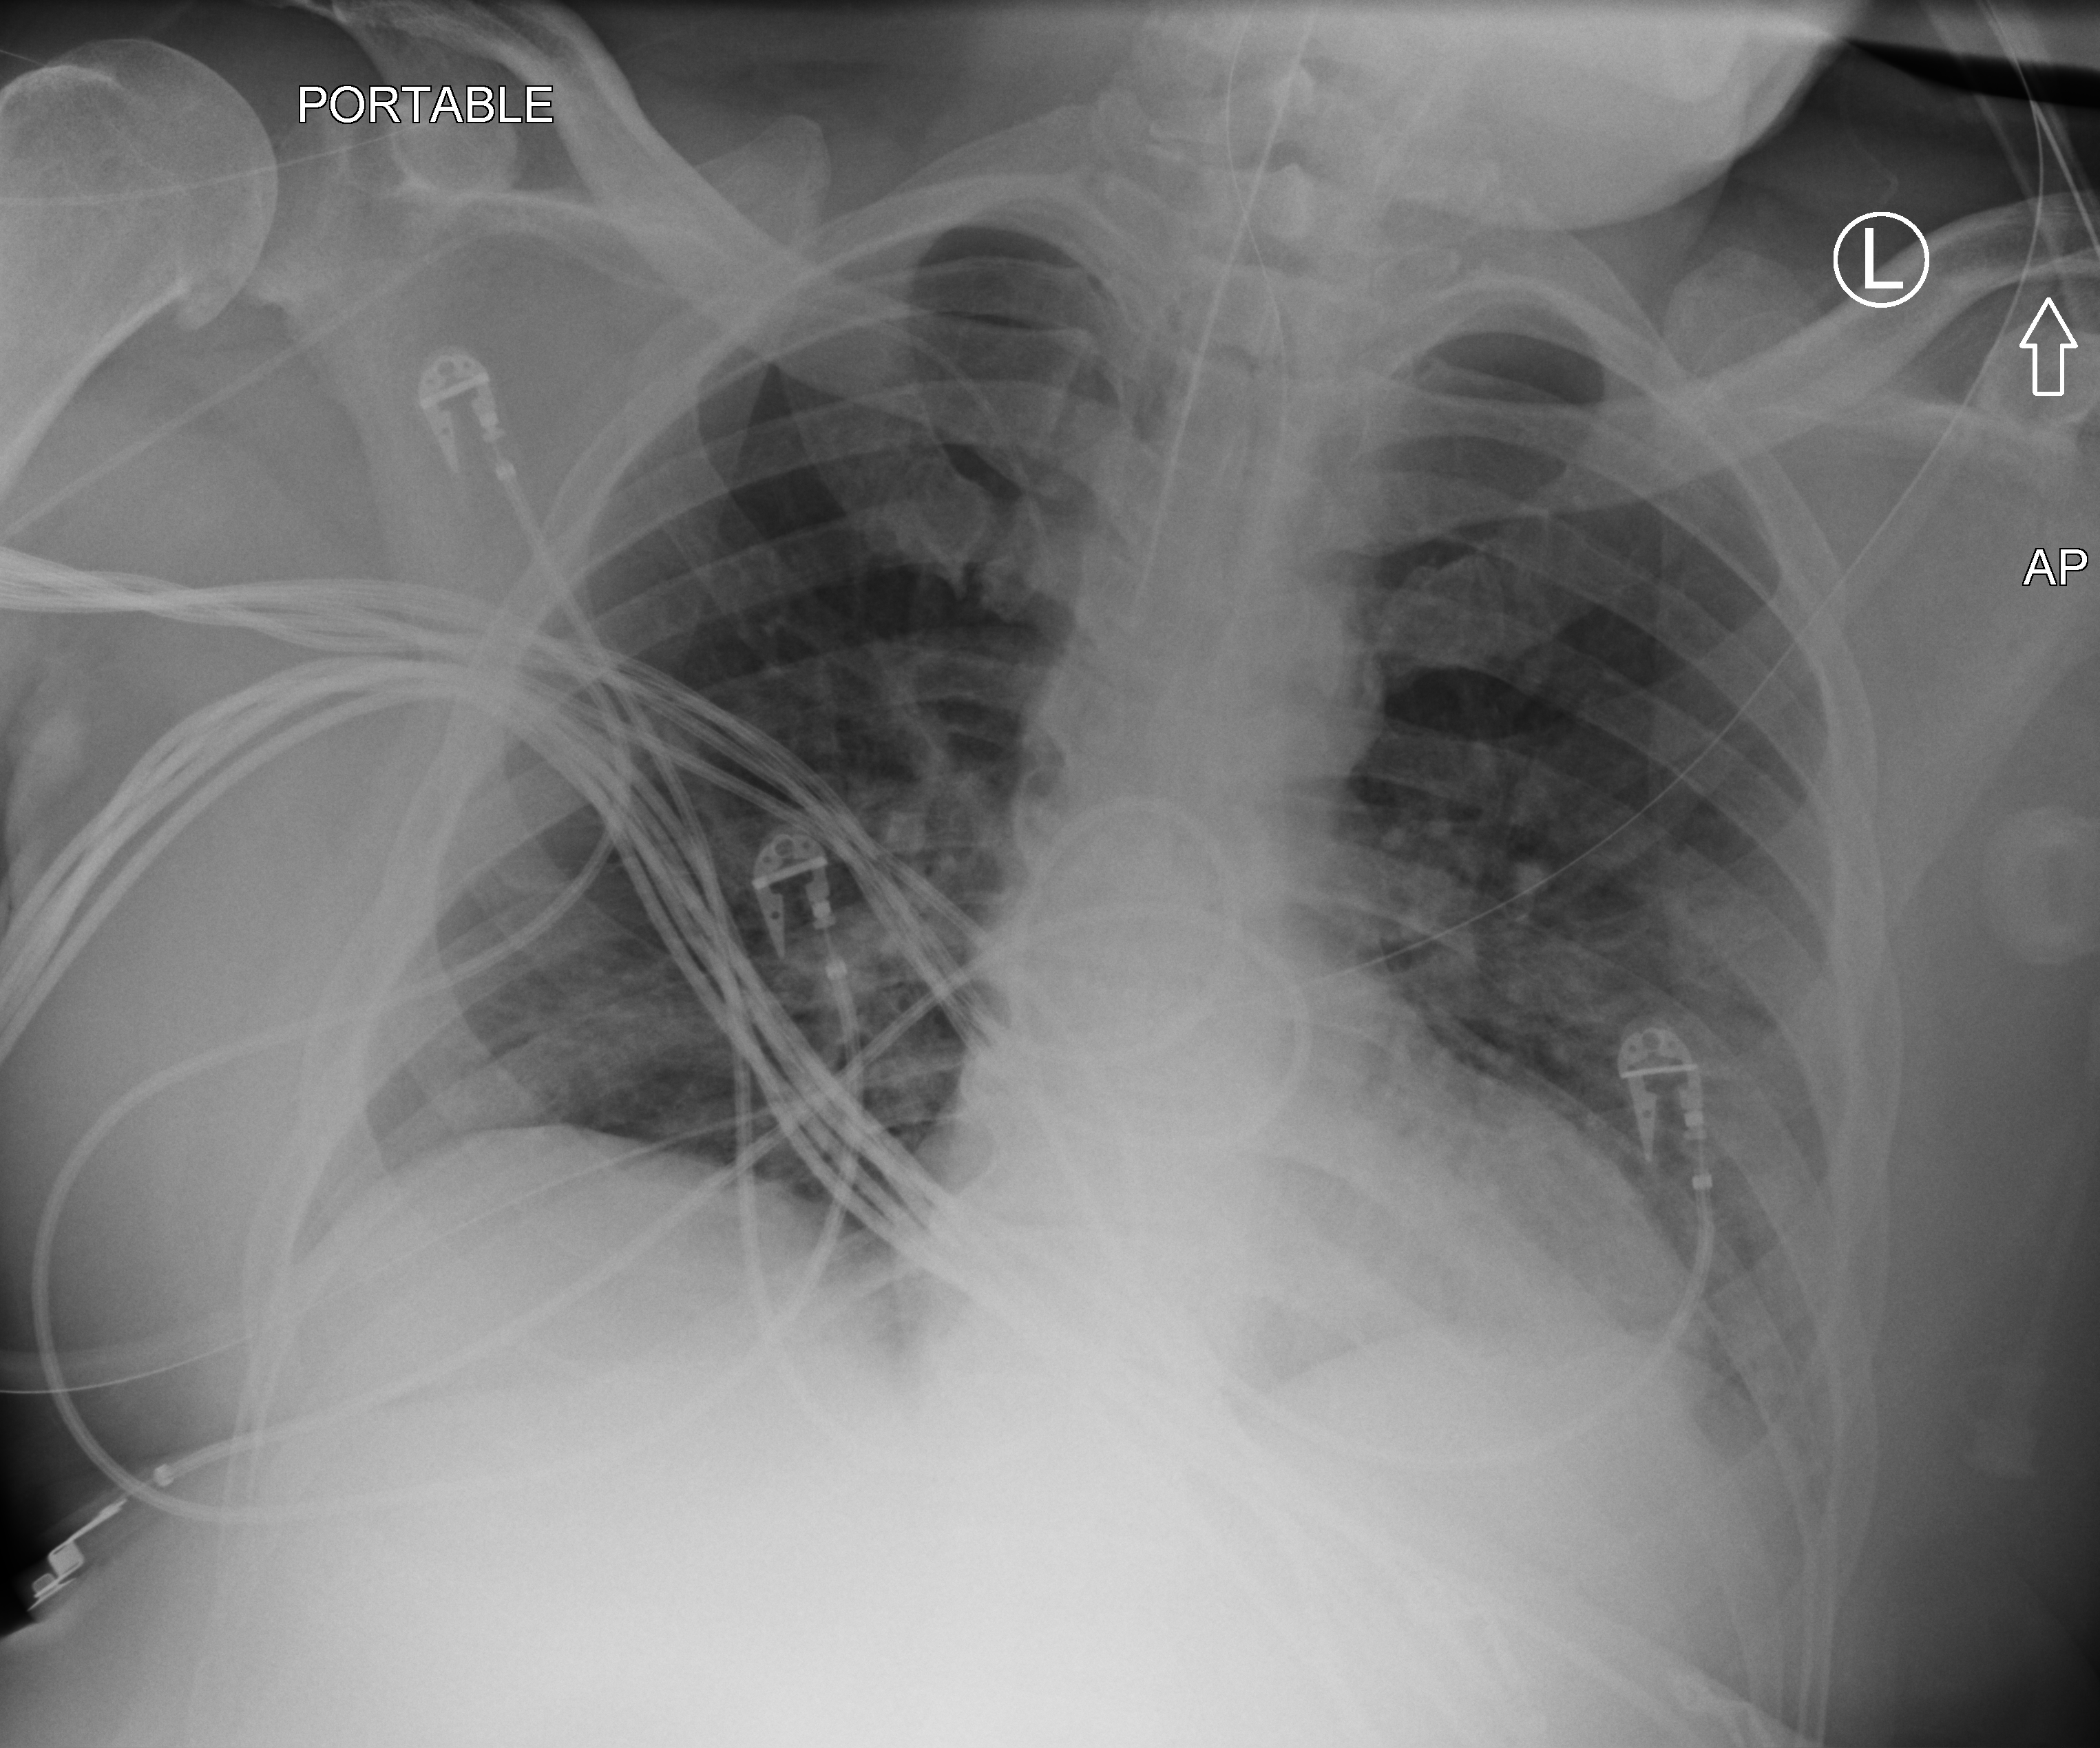
Chest X-ray (portable); anteroposterior (AP) projection. Patient hospitalised with COVID-19; male, aged 18–59 years.
Hospital-stay facts (about this admission, not read from this image; timing relative to this image not recorded): chronic kidney disease (admission record): no.